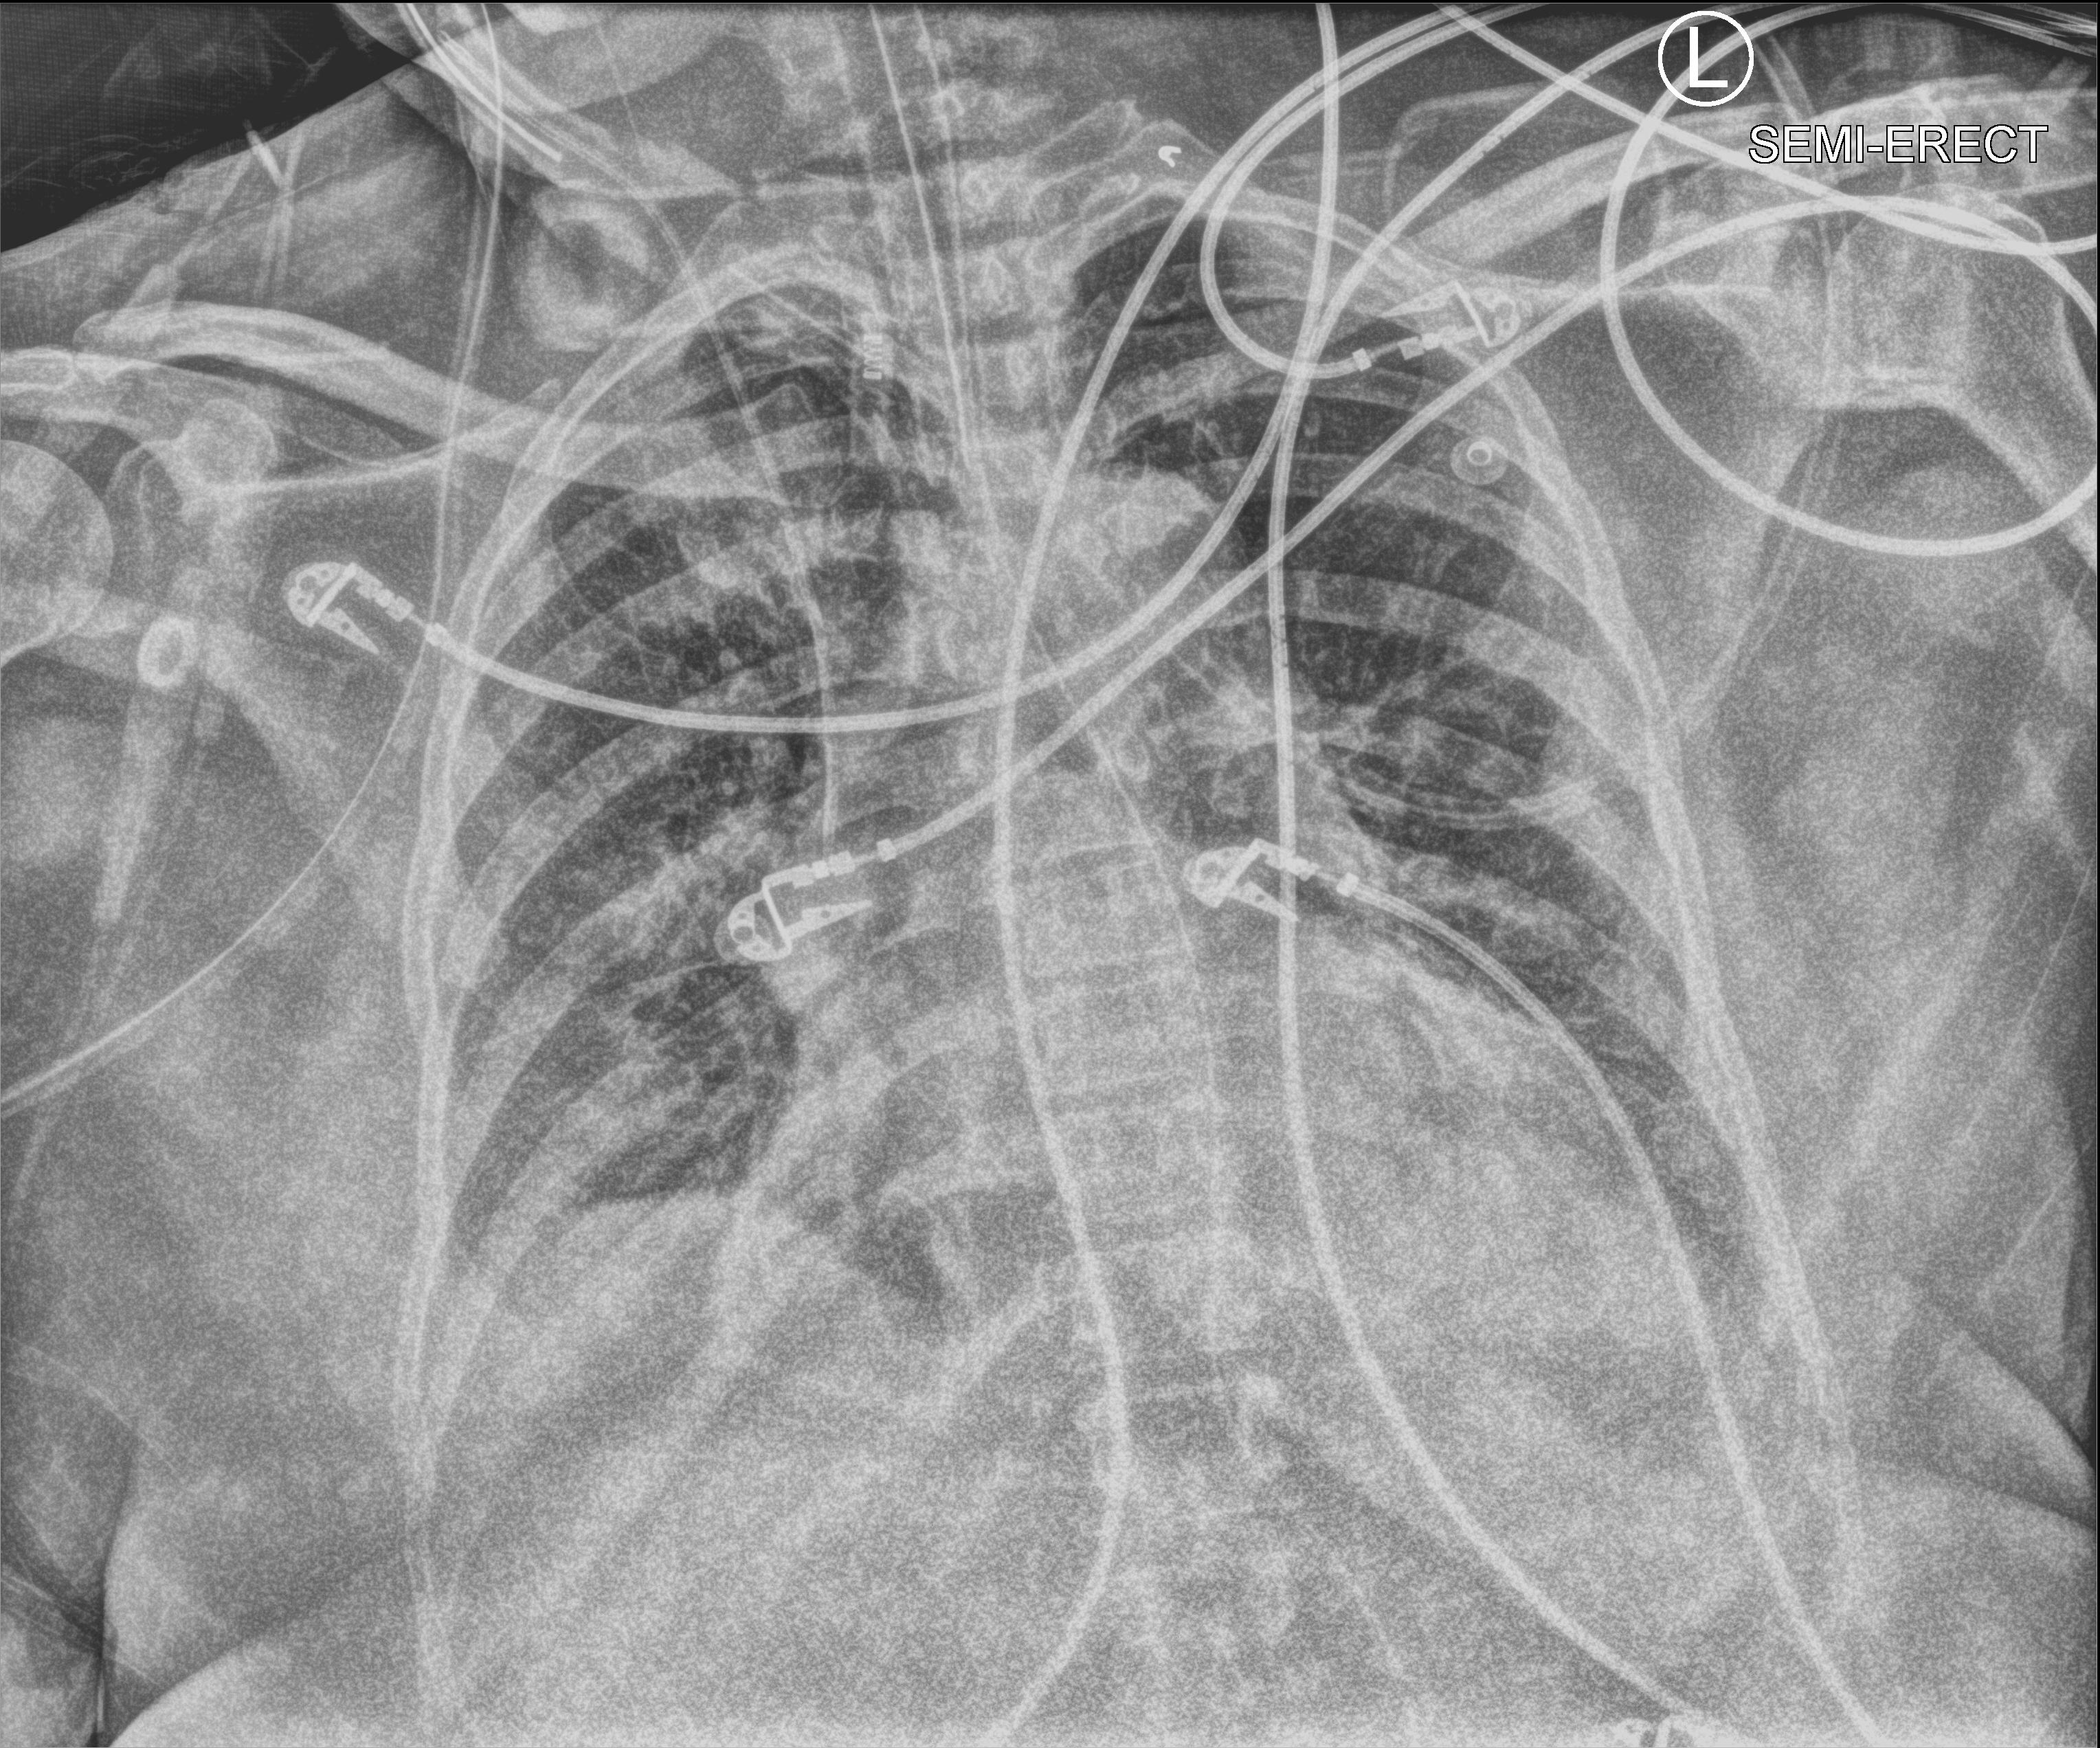
Chest X-ray (portable); anteroposterior (AP) projection. Patient hospitalised with COVID-19; female, aged 60–74 years.
Admission-level facts for this patient (not findings on this image; timing relative to this image not recorded): COPD (admission record): no.